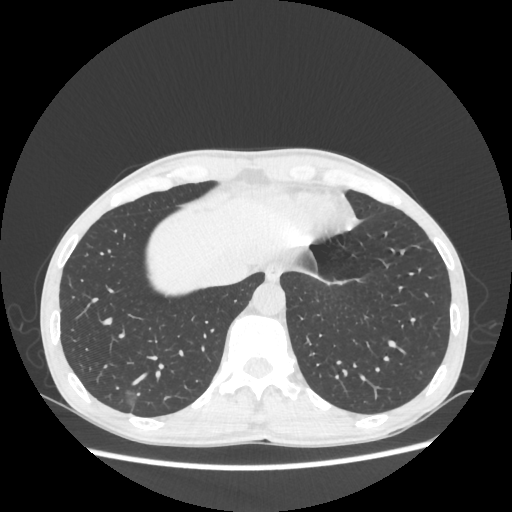
Chest CT, one axial slice; 100 kVp; lung window (W 1500 / L -600 HU); 1.25 mm slice thickness; 512 × 512 image matrix, field of view 360 × 360 mm. Patient: male, 60 years. From the clinical record (not read from this slice): clinical TNM (as recorded): T1c N0 M0.
Structures marked on this image (bounding box drawn by a radiologist):
- lung tumour (recorded histology: adenocarcinoma): bounding box (x1, y1, x2, y2) in pixels: (117, 386, 143, 421)